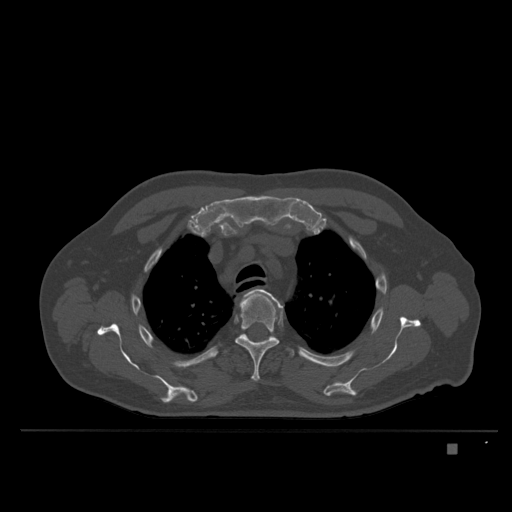
CT including the spine, one axial slice. Slice 287 of 435 in the series (ordered by position). Bone window (W 1800 / L 400 HU). 1.5 mm slice thickness. 512 × 512 image matrix, field of view 434 × 434 mm. Male patient, age 73 years. From the clinical record (not read from this slice): primary cancer: skin.
Outlined on this slice (semi-automatic segmentation, software-assisted and operator-edited):
- T3 vertebra: bounding box [x1, y1, x2, y2] px = [243, 289, 282, 308]
- T4 vertebra: [235, 294, 279, 382]
- T5 vertebra: [223, 334, 294, 356]